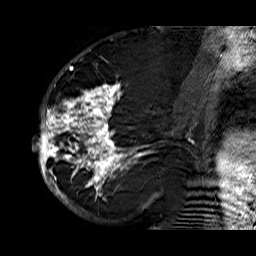
Breast MRI (dynamic contrast-enhanced), one sagittal slice; position 31 of 60 along the scan axis; dynamic contrast-enhanced series, time point 2 of 6 at this slice position (early post-contrast); 1.5 T; TE 6.3 ms, TR 32.9 ms; 4 mm slice thickness; 256 × 256 image matrix, field of view 200 × 200 mm. Female patient. From the clinical record (not read from this slice): setting: breast cancer imaged before/during neoadjuvant chemotherapy; receptor status: HR-positive, HER2-negative.
Annotated regions visible in this slice (semi-automatically segmented with operator editing):
- analysis volume of interest (the breast-tissue region the enhancement analysis was run in; not a lesion): box from (x=33, y=74) to (x=176, y=210) px
- tumour enhancement mask (voxels above the 100 % enhancement threshold inside the analysis volume of interest): (x=33, y=74)–(x=173, y=210)